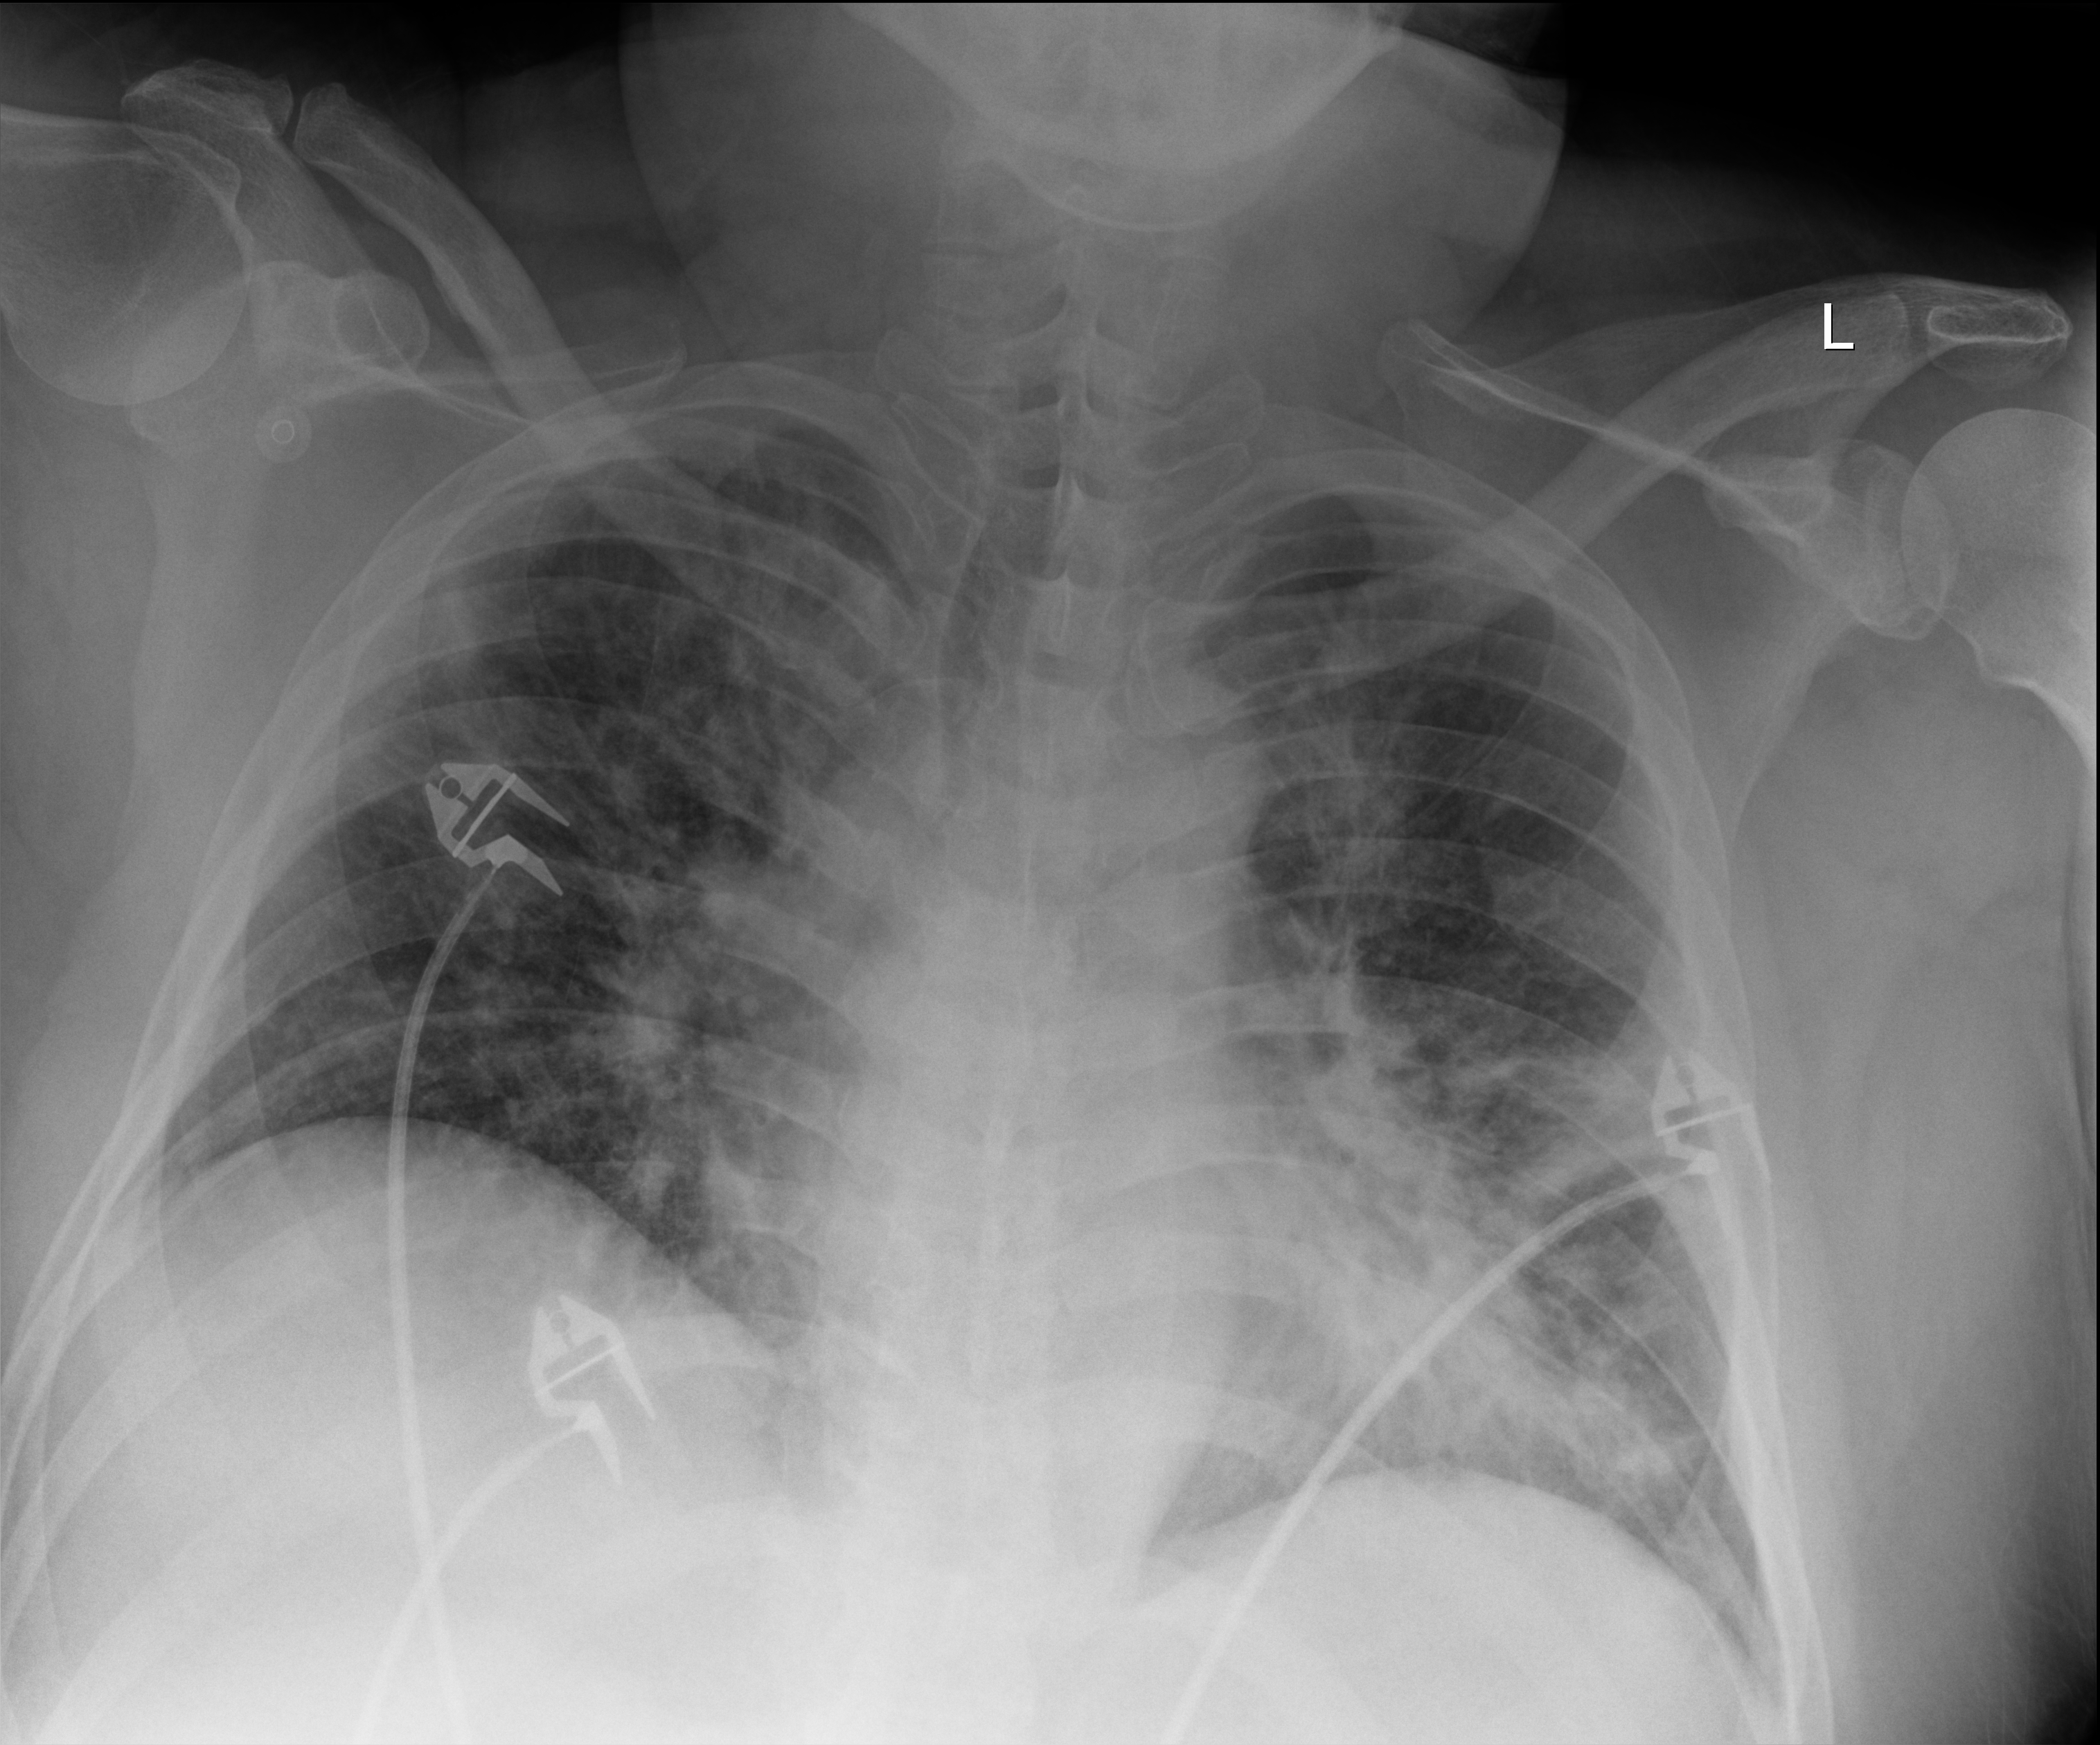
Portable chest radiograph; anteroposterior (AP) projection. Male patient hospitalised with COVID-19, age 18–59 years.
Admission-level facts for this patient (not findings on this image; timing relative to this image not recorded): length of hospital stay: 22 days; admitted to intensive care during this hospital stay: no; mechanically ventilated during this hospital stay: no.